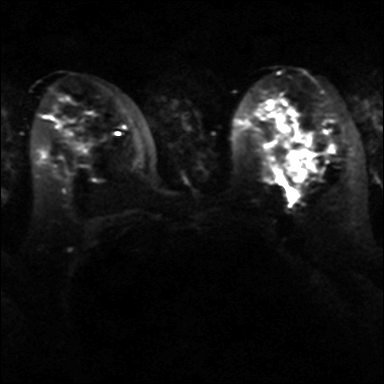
Breast MRI, one axial slice; position 20 of 40 along the scan axis; diffusion-weighted series; image 2 of 4 stored at this slice position (different b-values; order by instance number); 3 T; 384 × 384 image matrix, field of view 320 × 320 mm. Female patient.
Outlined on this slice (outlined manually by an expert reader):
- tumour on diffusion-weighted imaging: bounding box [x1, y1, x2, y2] px = [283, 148, 316, 182]